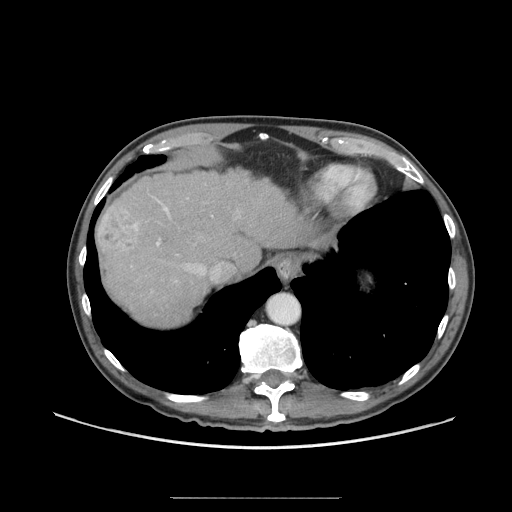
Contrast-enhanced abdominal CT (liver protocol), one axial slice; position 55 of 71 along the scan axis; reconstruction kernel STANDARD; soft-tissue window (W 400 / L 40 HU); 512 × 512 image matrix, field of view 400 × 400 mm. From the clinical record (not read from this slice): diagnosis: hepatocellular carcinoma (patient treated with transarterial chemoembolisation; whether this scan precedes or follows treatment is not stated here); TNM stage (as recorded): Stage-I; Child-Pugh class: A; tumour nodularity: uninodular.
Outlined on this slice (semi-automatically segmented with operator editing):
- abdominal aorta: bounding box (x1, y1, x2, y2) in pixels: (267, 294, 299, 324)
- liver parenchyma outside the tumour (the mass and vessels are separate outlines, so this box may not span the whole liver): (96, 170, 312, 326)
- mass: (96, 200, 140, 261)
- liver vessels: (155, 198, 220, 282)